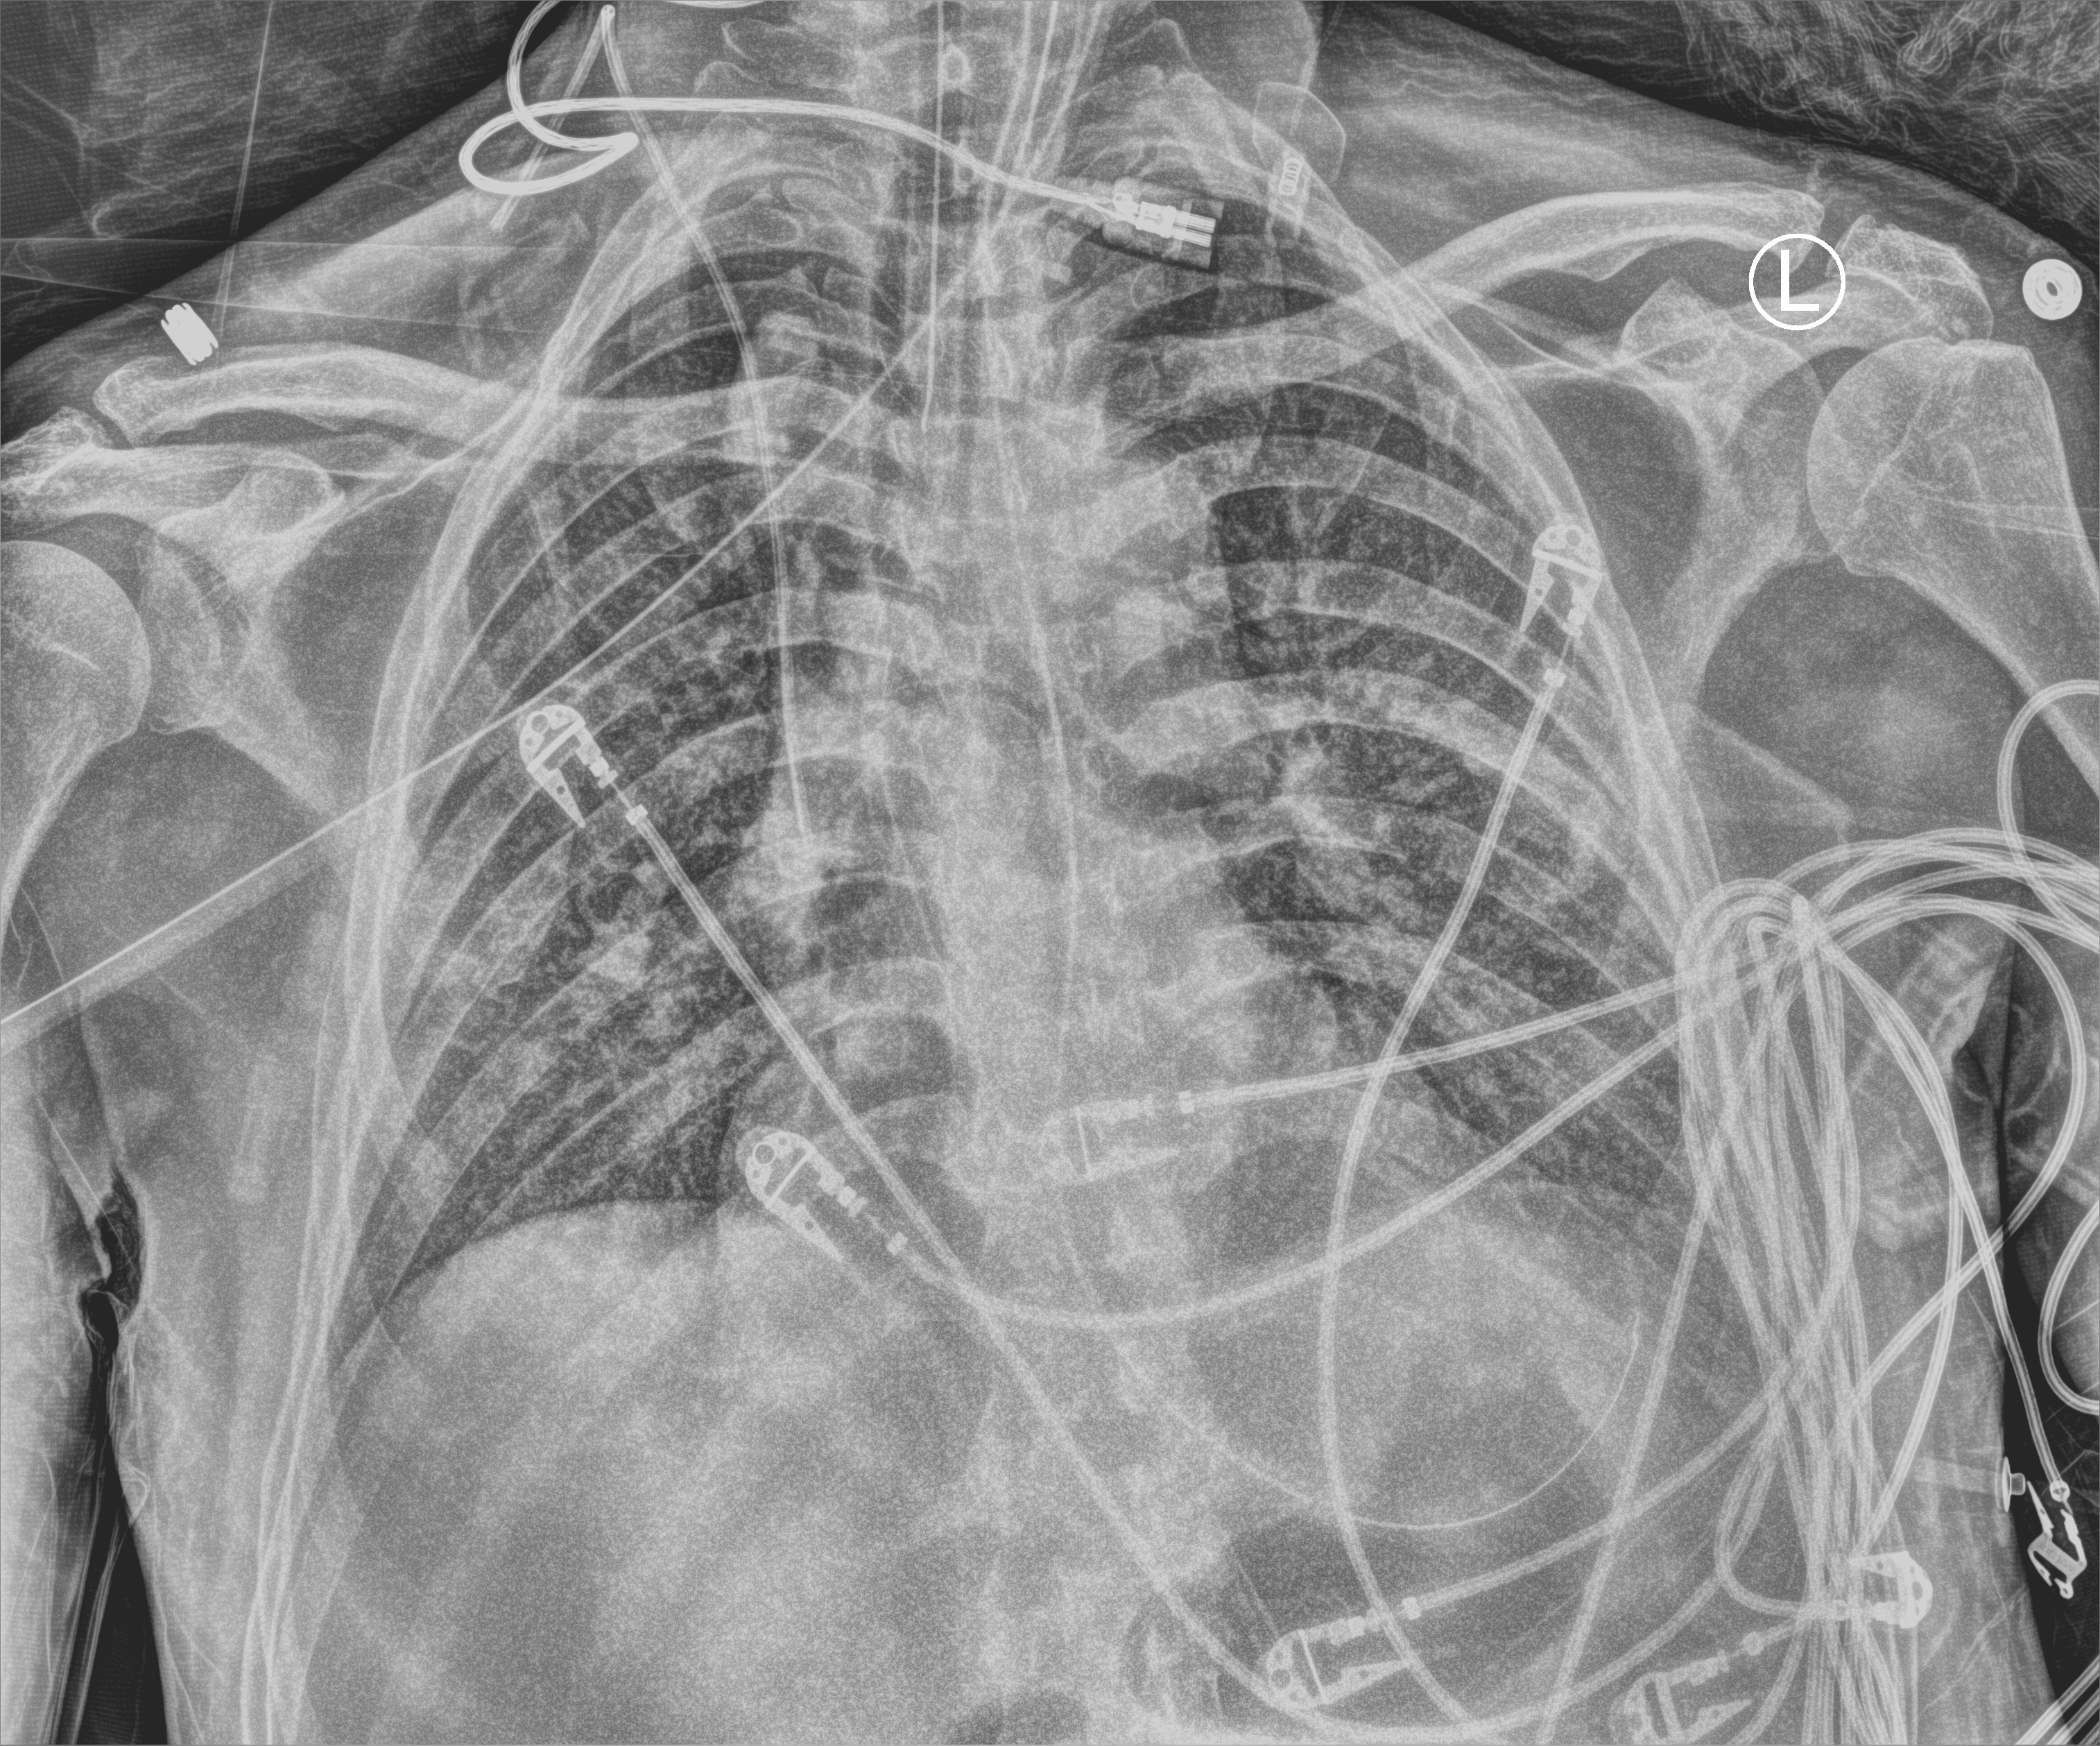
Portable chest radiograph; anteroposterior (AP) projection. Male patient hospitalised with COVID-19, age 60–74 years.
Hospital-stay facts (about this admission, not read from this image; timing relative to this image not recorded):
- chronic kidney disease (admission record): no
- mechanically ventilated during this hospital stay: yes